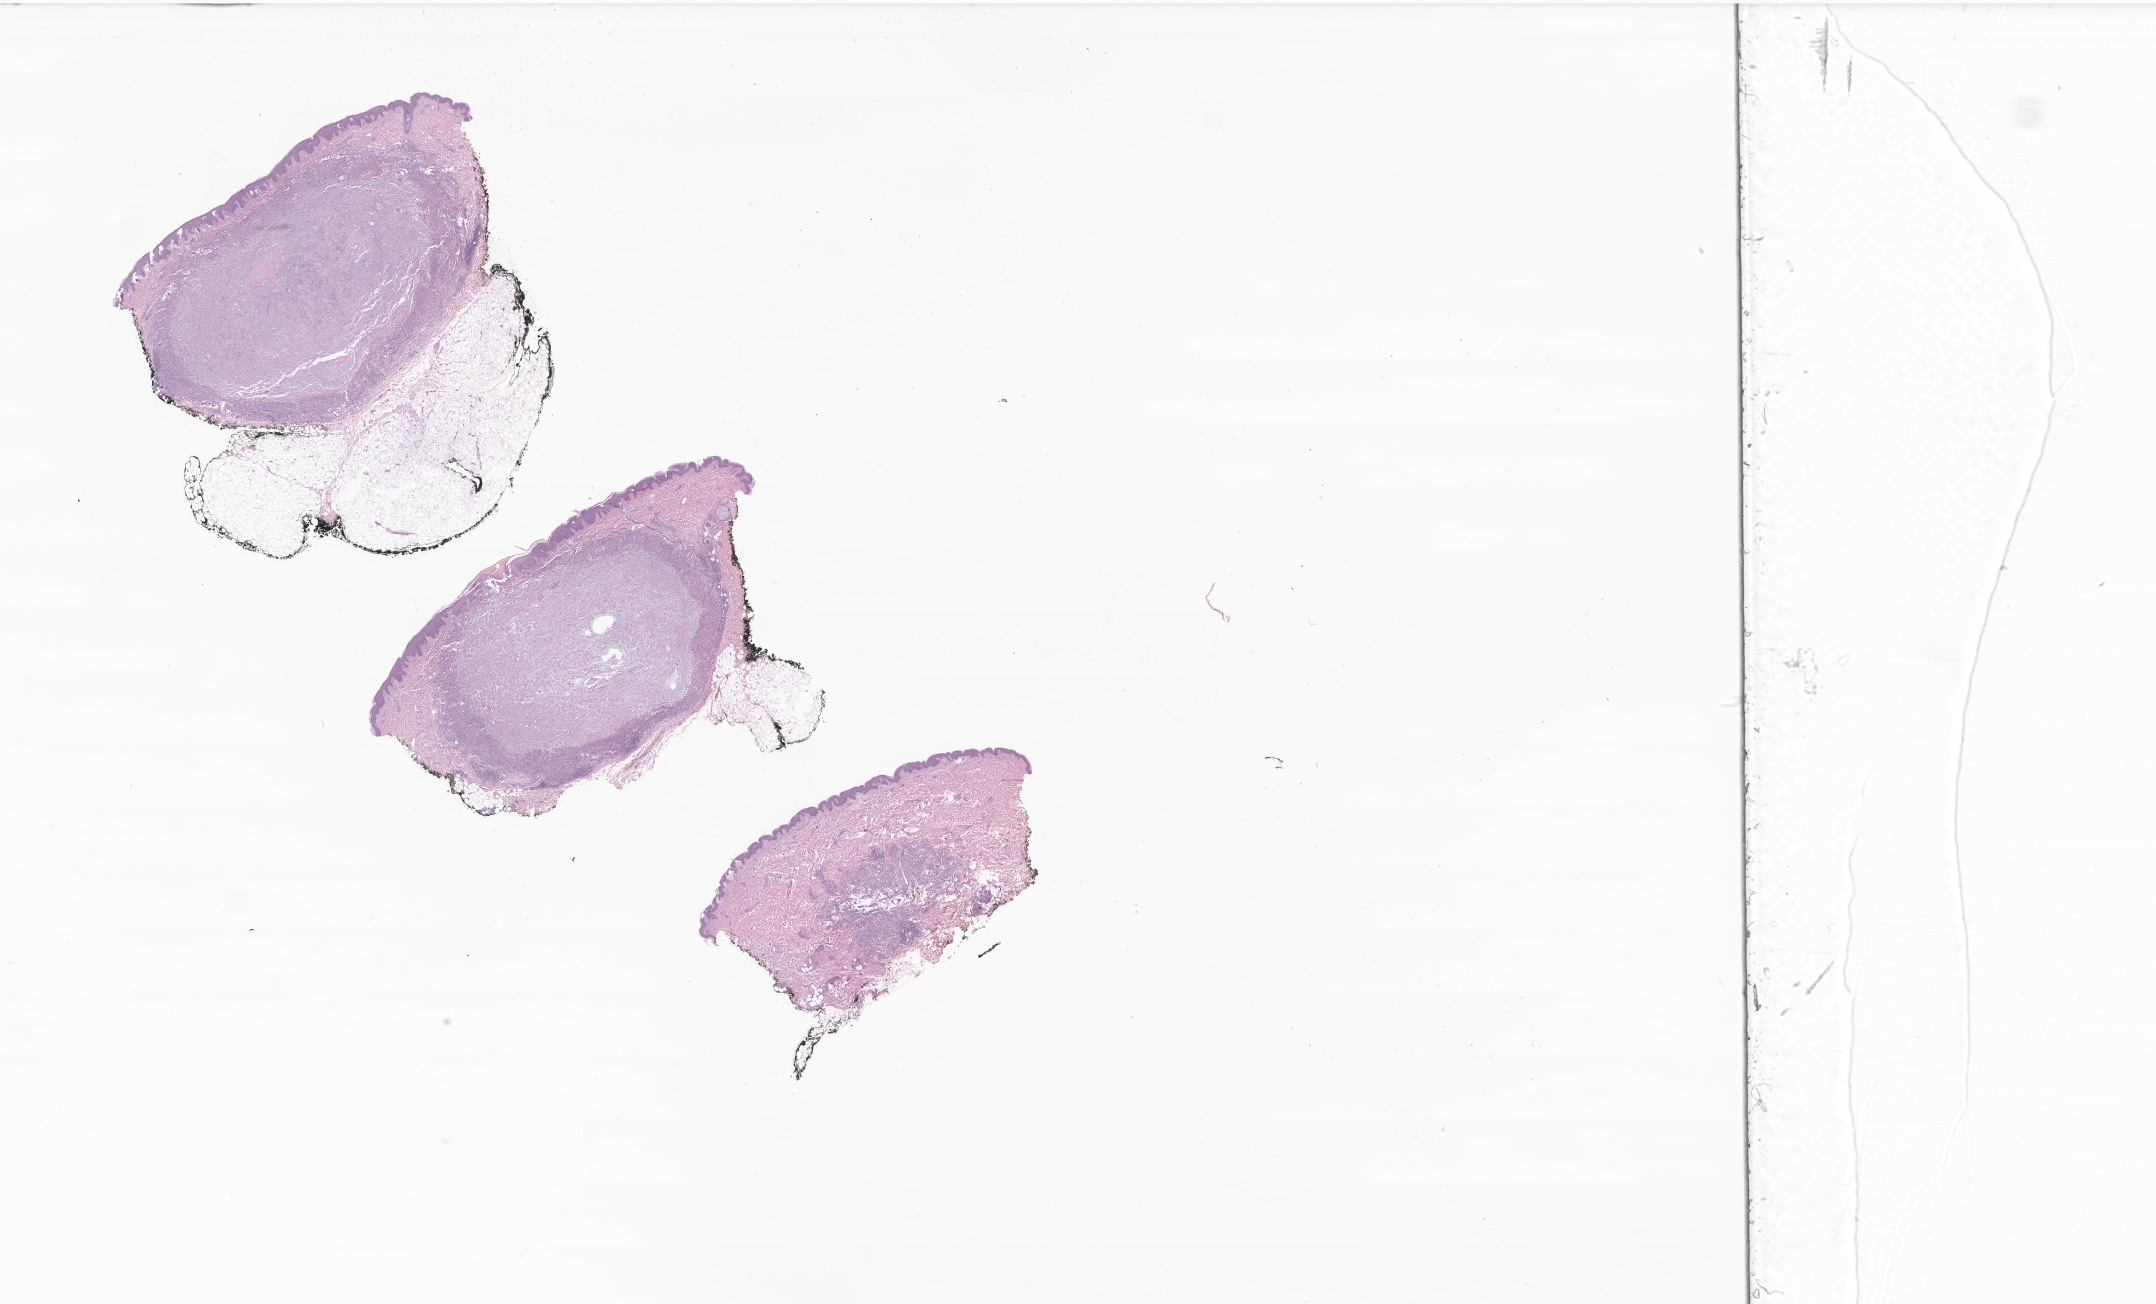
Hematoxylin and eosin (H&E) whole-slide image of tumor tissue from the upper limb — a low-resolution overview of the entire scanned area, about 36.4 x 22.0 mm. Formalin-fixed, paraffin-embedded (FFPE) tissue. Patient: female, age 207 months (17 years 3 months).
• diagnosis: Epithelioid sarcoma, NOS